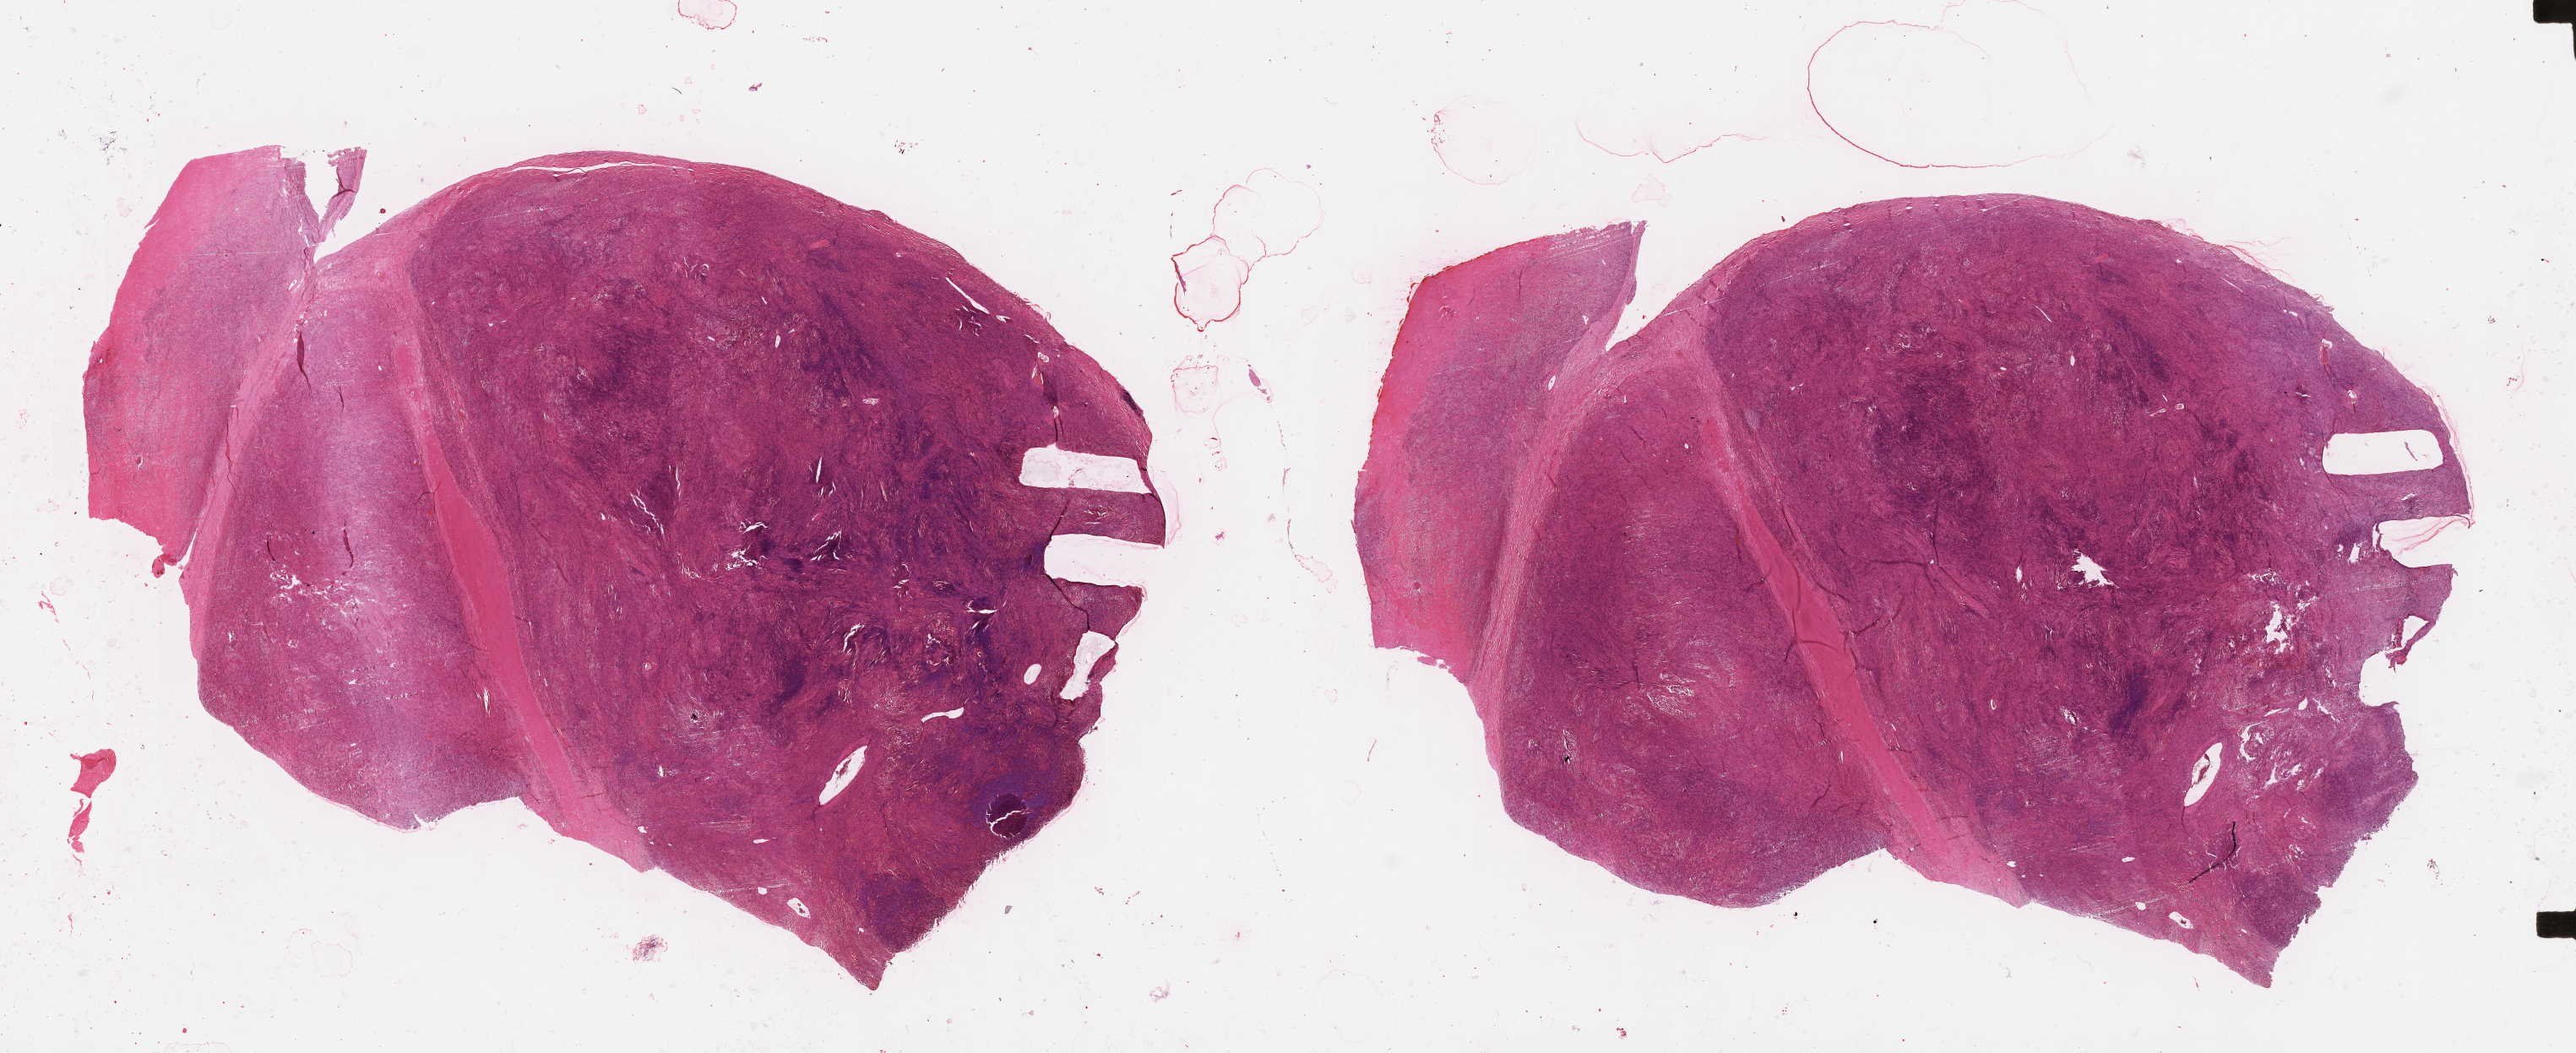
H&E-stained whole-slide image, whole scanned area (about 49.1 x 20.1 mm) shown as a low-resolution overview, tumour tissue sample. 62-year-old male patient.
• primary tumour site (as recorded): chest
• patient diagnosis (cohort enrolment): sarcoma (site not recorded at cohort level)